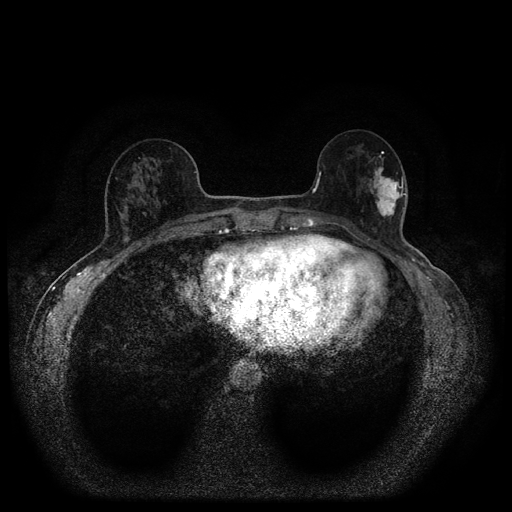
Breast MRI (dynamic contrast-enhanced, multi-phase), one axial slice. Position 40 of 116 along the scan axis. Dynamic contrast-enhanced series, time point 2 of 5 at this slice position (early post-contrast). 1.5 T. TE 2.7 ms, TR 5.4 ms. 512 × 512 image matrix, field of view 330 × 330 mm. Female patient, age 56 years.
Annotated regions visible in this slice (semi-automatic segmentation, software-assisted and operator-edited):
- breast lesion (labelled 'tumour' in the annotation; benign lesions carry a separate 'benign' label): bounding box [x1, y1, x2, y2] px = [366, 151, 408, 222]